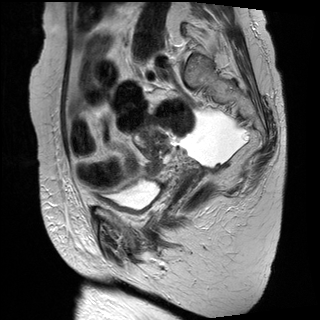
Pelvic MRI for cervical cancer, one sagittal slice. T2-weighted. 1.5 T. TE 89 ms, TR 2930 ms. 4 mm slice thickness. 320 × 320 image matrix. Female patient, age 61 years.
Annotated regions visible in this slice (outlined manually by an expert reader):
- uterus and cervix: bounding box [x1, y1, x2, y2] px = [139, 129, 198, 181]